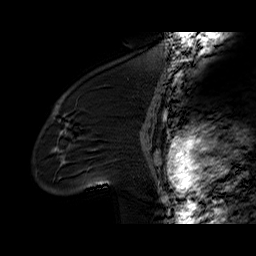
Breast MRI (dynamic contrast-enhanced), one sagittal slice; position 43 of 60 along the scan axis; dynamic contrast-enhanced series, time point 2 of 6 at this slice position (early post-contrast); 1.5 T; TE 6.2 ms, TR 32.4 ms; 4 mm slice thickness; 256 × 256 image matrix, field of view 200 × 200 mm. Female patient. From the clinical record (not read from this slice): setting: breast cancer imaged before/during neoadjuvant chemotherapy; receptor status: triple-negative.
Outlined on this slice (semi-automatically segmented with operator editing):
- analysis volume of interest (the breast-tissue region the enhancement analysis was run in; not a lesion): box from (x=36, y=97) to (x=134, y=195) px
- tumour enhancement mask (voxels above the 100 % enhancement threshold inside the analysis volume of interest): (x=55, y=106)–(x=66, y=164)